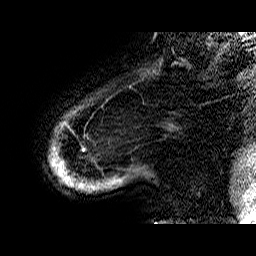
Breast MRI (dynamic contrast-enhanced), one sagittal slice; position 4 of 60 along the scan axis; dynamic contrast-enhanced series, time point 2 of 6 at this slice position (early post-contrast); 1.5 T; TE 6.4 ms, TR 32.9 ms; 4 mm slice thickness; 256 × 256 image matrix, field of view 200 × 200 mm. Female patient. Case-level facts recorded for this patient, not image findings: setting: breast cancer imaged before/during neoadjuvant chemotherapy; receptor status: HR-positive, HER2-negative.
Structures marked on this image (semi-automatically segmented with operator editing):
- analysis volume of interest (the breast-tissue region the enhancement analysis was run in; not a lesion): bounding box [x1, y1, x2, y2] px = [50, 98, 154, 193]
- tumour enhancement mask (voxels above the 100 % enhancement threshold inside the analysis volume of interest): [51, 123, 84, 183]